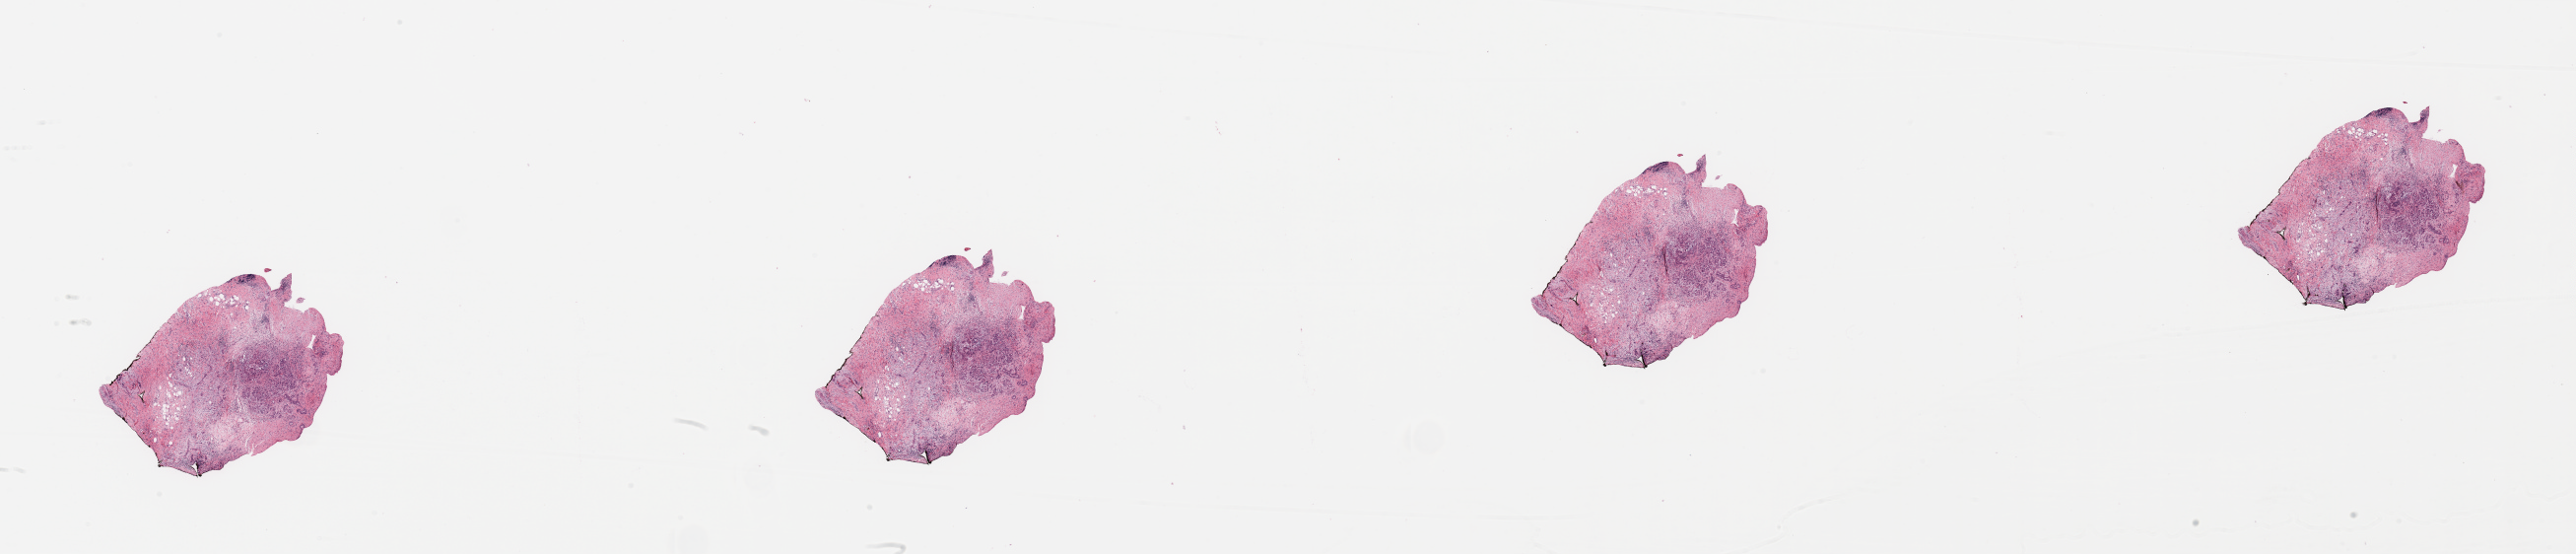
H&E whole-slide image, low-resolution overview of the scanned area, about 41.3 x 8.9 mm (acquisition: 20x scan); tumour tissue sample, sampled site: pancreas. Patient: male, age 65 years. Histologic grade: G3 (poorly differentiated). Pathologist review of this section (percent, as recorded): tumour nuclei 10%, necrosis 0%.
Primary tumour site (as recorded): head. Diagnosis: Infiltrating duct carcinoma, NOS. AJCC pathologic stage: IIB.